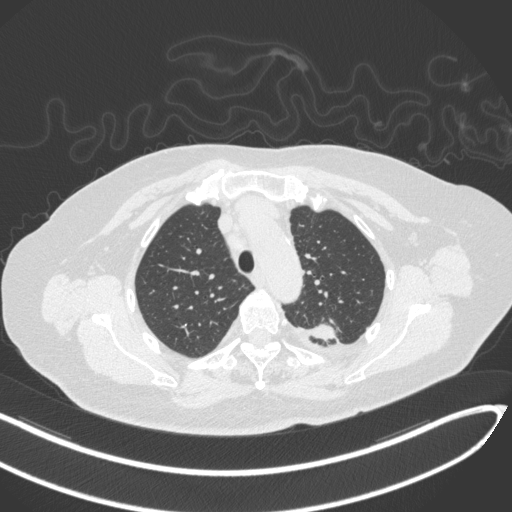
Chest CT, one axial slice; 120 kVp; lung window (W 1500 / L -600 HU); 1 mm slice thickness; 512 × 512 image matrix, field of view 400 × 400 mm. Female patient, age 76 years. From the clinical record (not read from this slice): clinical TNM (as recorded): T1c N0 M0.
Annotated regions visible in this slice (bounding box drawn by a radiologist):
- lung tumour (recorded histology: adenocarcinoma): bounding box (x1, y1, x2, y2) in pixels: (308, 319, 337, 344)